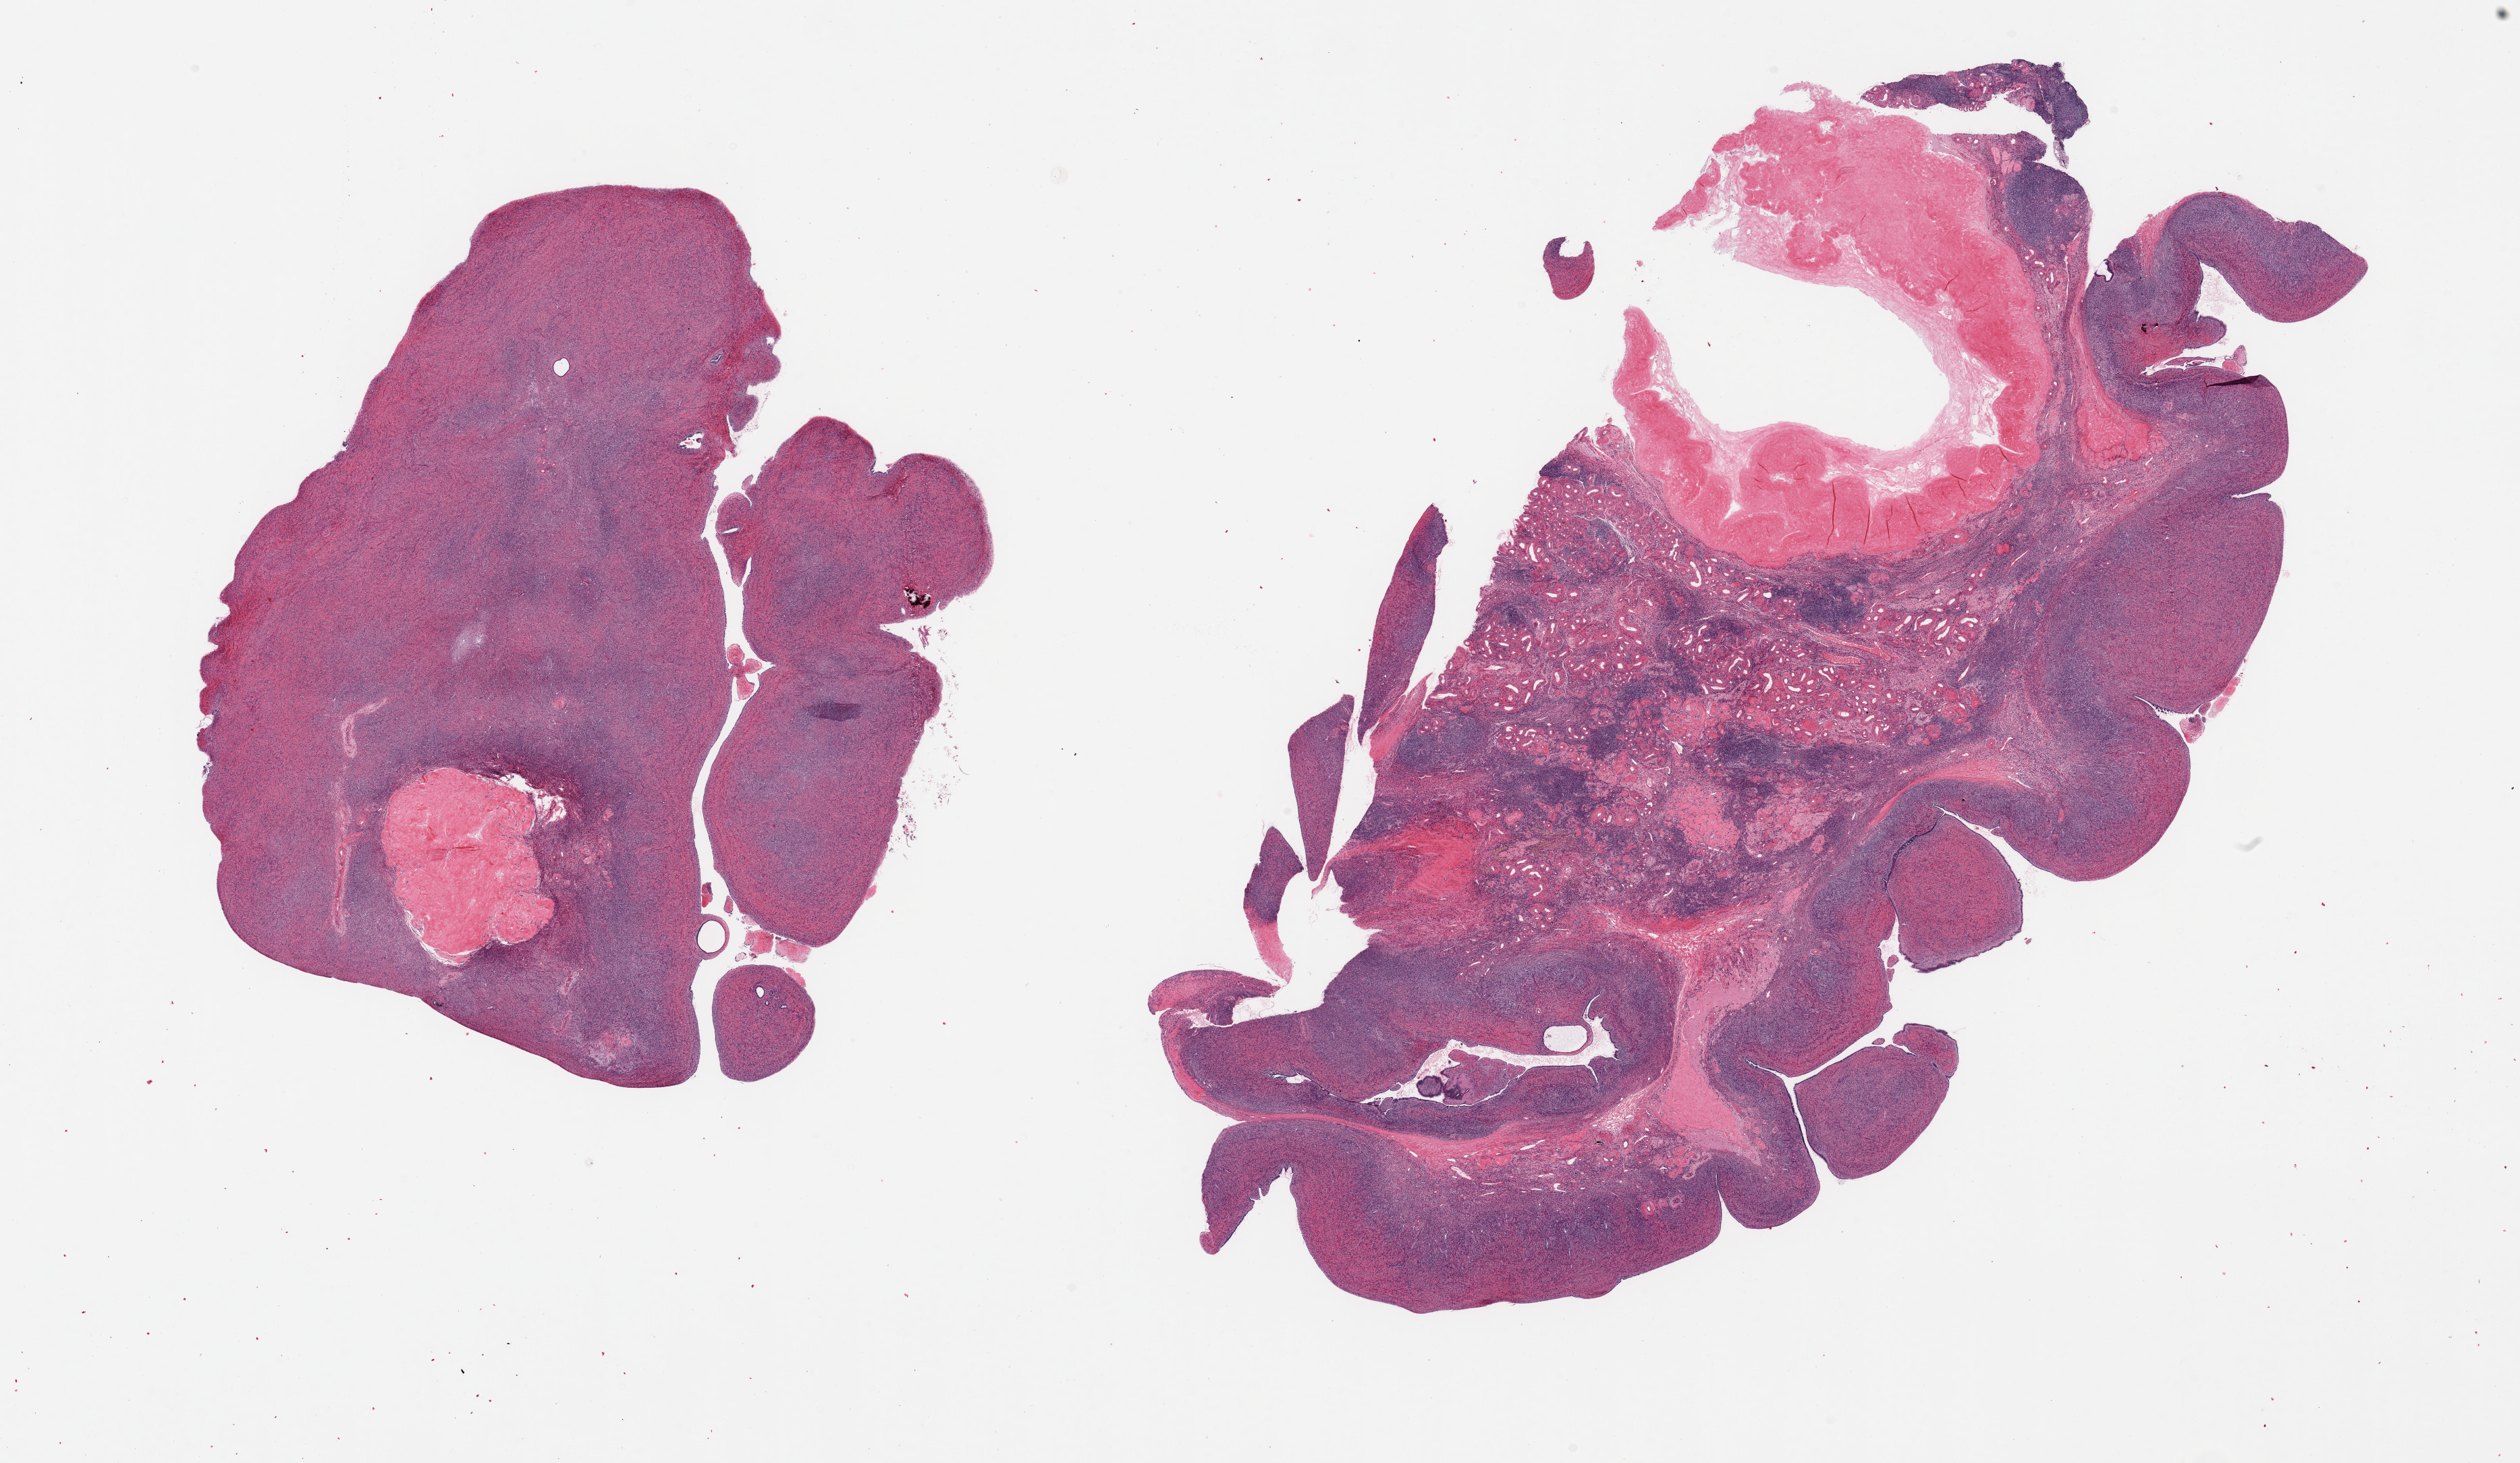
Haematoxylin and eosin whole-slide image, a low-resolution overview of the entire scanned area, about 29.5 x 17.1 mm (from a 20x scan), PAXgene-fixed, paraffin-embedded tissue, sampled site (target tissue): ovary, donor tissue sample. Donor: female.
Reviewer comment on this tissue sample: 2 pieces, post menopausal atrophy/involutional changes.